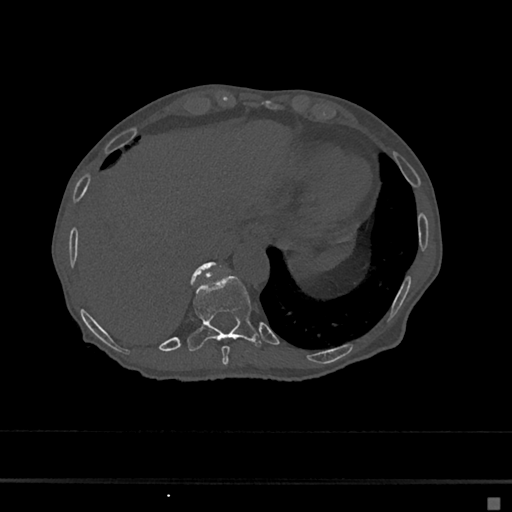
CT including the spine, one axial slice; position 230 of 797 along the scan axis; 120 kVp; bone window (W 1800 / L 400 HU); 512 × 512 image matrix, field of view 360 × 360 mm. Female patient, age 68 years. From the clinical record (not read from this slice): primary cancer: renal.
Annotated regions visible in this slice (semi-automatically segmented with operator editing):
- T10 vertebra: bounding box [x1, y1, x2, y2] px = [188, 275, 260, 351]
- T11 vertebra: [192, 261, 218, 279]
- T9 vertebra: [221, 346, 230, 365]